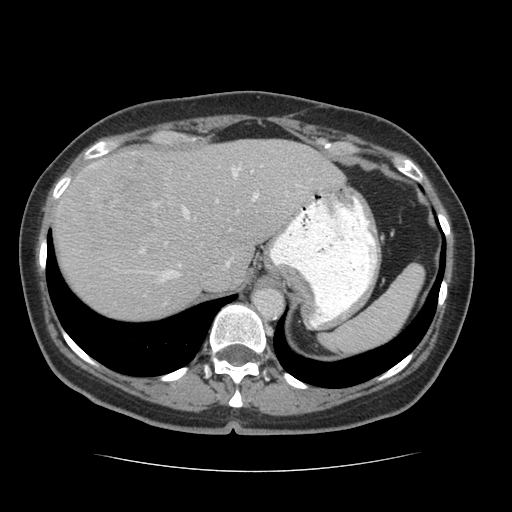
Contrast-enhanced abdominal CT (liver protocol), one axial slice; slice 51 of 75 in the series (ordered by position); soft-tissue window (W 400 / L 40 HU); 2.5 mm slice thickness; 512 × 512 image matrix, field of view 360 × 360 mm. Case-level facts recorded for this patient, not image findings: diagnosis: hepatocellular carcinoma (patient treated with transarterial chemoembolisation; whether this scan precedes or follows treatment is not stated here); TNM stage (as recorded): Stage-I; Child-Pugh class: A; tumour differentiation: moderately differentiated.
Annotated regions visible in this slice (semi-automatic segmentation, software-assisted and operator-edited):
- abdominal aorta: bounding box <253,287,283,317> (left, top, right, bottom; pixels)
- liver parenchyma outside the tumour (the mass and vessels are separate outlines, so this box may not span the whole liver): <52,140,358,318>
- mass: <65,152,174,253>
- liver vessels: <57,167,357,282>